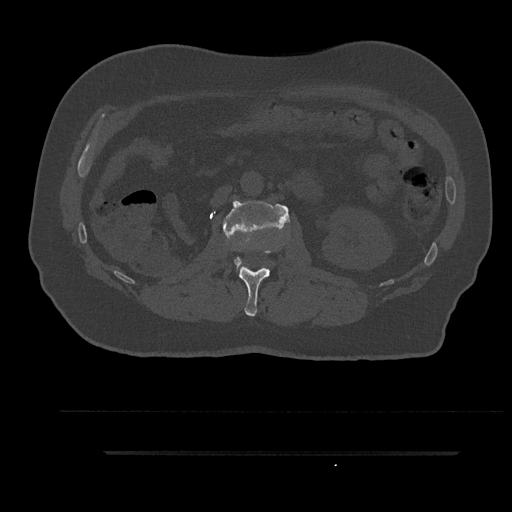
CT including the spine, one axial slice; slice 145 of 797 in the series (ordered by position); 120 kVp; bone window (W 1800 / L 400 HU); 512 × 512 image matrix, field of view 432 × 432 mm. Male patient, age 63 years. From the clinical record (not read from this slice): primary cancer: renal; vertebrae with lytic lesions (as recorded): T8.
Structures marked on this image (semi-automatic segmentation, software-assisted and operator-edited):
- L1 vertebra: bounding box <238,250,275,316> (left, top, right, bottom; pixels)
- L2 vertebra: <223,200,289,267>